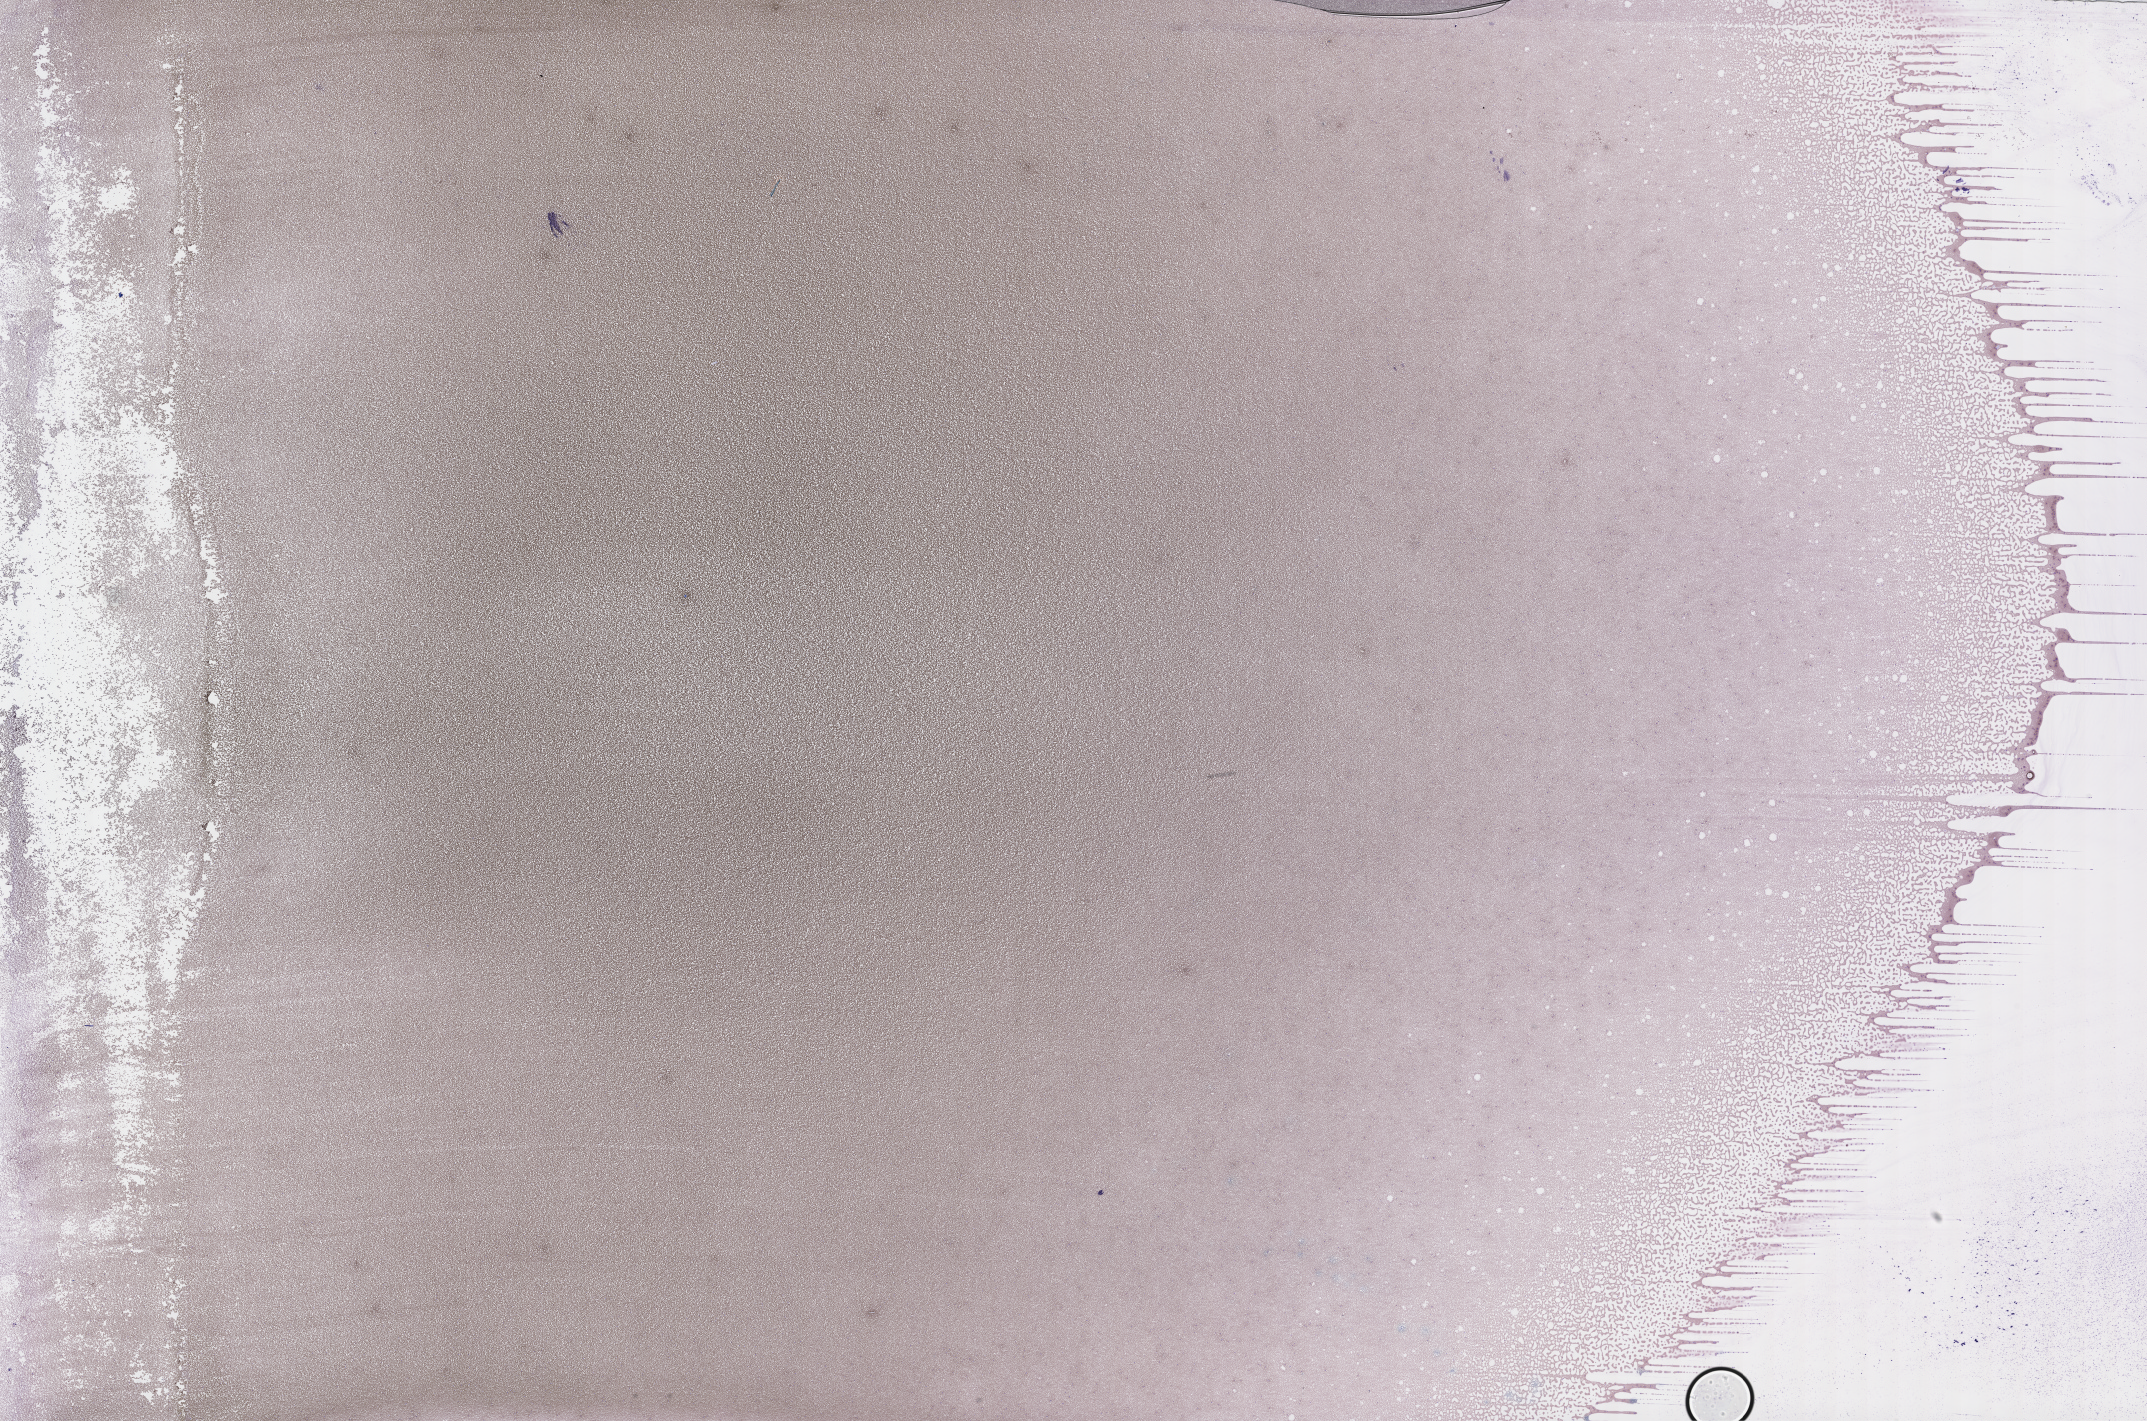
Wright–Giemsa-stained whole blood smear, whole-slide image, low-resolution overview of the scanned area, about 34.7 x 23.0 mm. Patient: male.
* patient diagnosis: Plasma Cell Myeloma